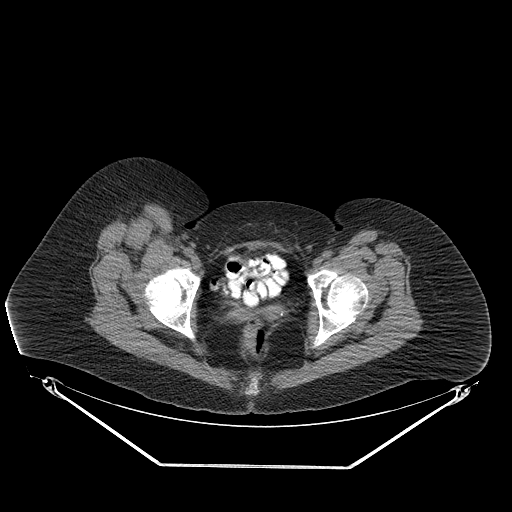
CT of an extremity soft-tissue mass (from a PET/CT study), one axial slice; reconstruction kernel STANDARD; 140 kVp; soft-tissue window (W 400 / L 40 HU); 512 × 512 image matrix, field of view 500 × 500 mm. Female patient. Case-level facts recorded for this patient, not image findings: histological type: malignant solitary fibrous tumor; grade: intermediate; site of the primary tumour: right thigh.
Structures marked on this image (expert contour drawn on MRI and transferred to this co-registered scan by the dataset authors):
- gross tumour volume including surrounding oedema: bounding box <116,221,142,243> (left, top, right, bottom; pixels)